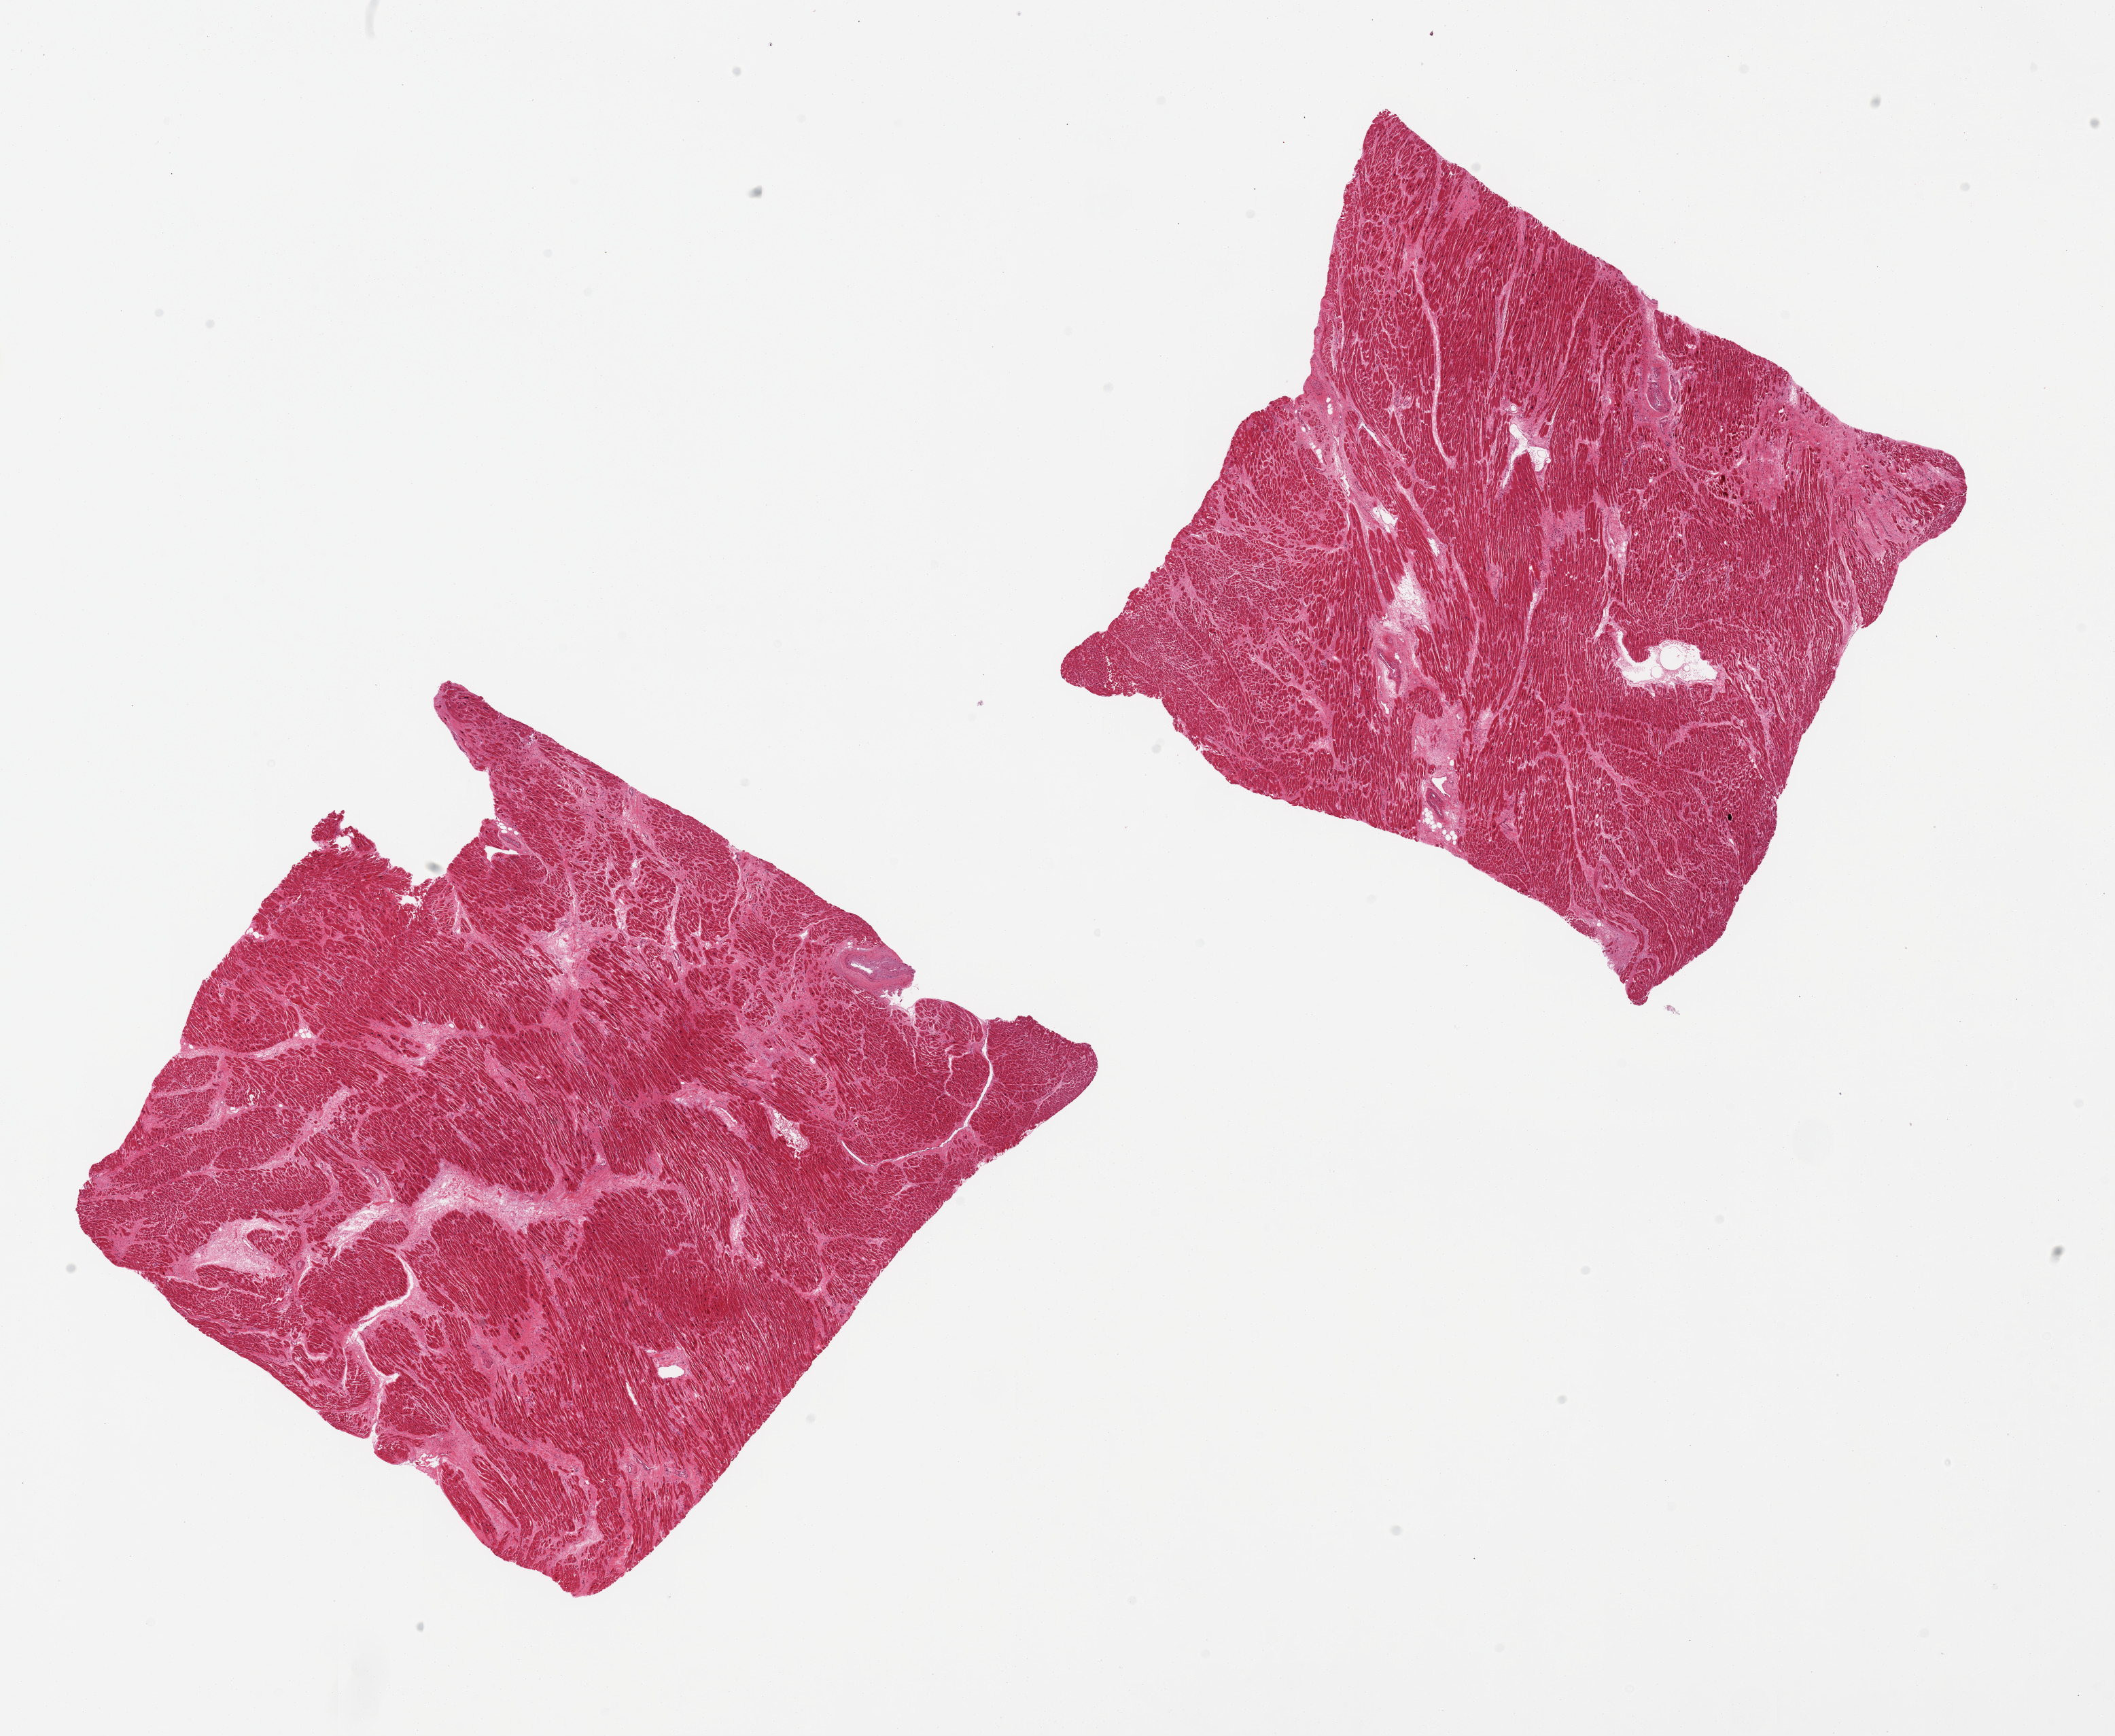
Digitized hematoxylin and eosin (H&E)-stained section — whole scanned area (about 24.6 x 20.2 mm, slide scanned at 20x) shown as a low-resolution overview; PAXgene-fixed, paraffin-embedded tissue; sampled site (target tissue): heart; tissue donor sample.
* review note (as recorded): 2 pieces, patcy interstitial fibrosis, remoted infarct, moderate ischemic damage